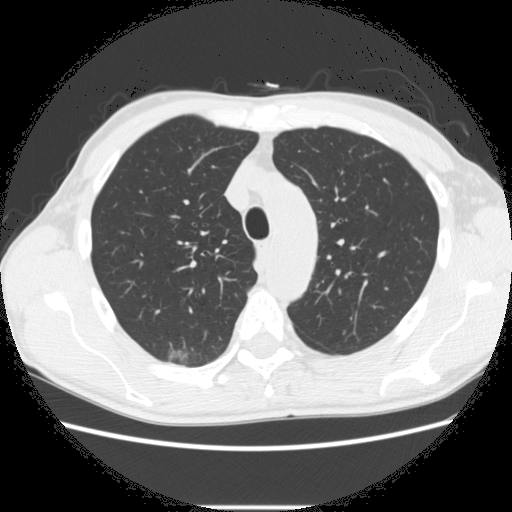
Low-dose screening chest CT, one axial slice; slice 211 of 282 in the series (ordered by position); reconstruction kernel STANDARD; 120 kVp; lung window (W 1500 / L -600 HU); 2.5 mm slice thickness; 512 × 512 image matrix, field of view 360 × 360 mm.
Outlined on this slice (outlined manually by an expert reader):
- lesion 1 (tumor, upper lobe of right lung): box from (x=170, y=350) to (x=187, y=361) px